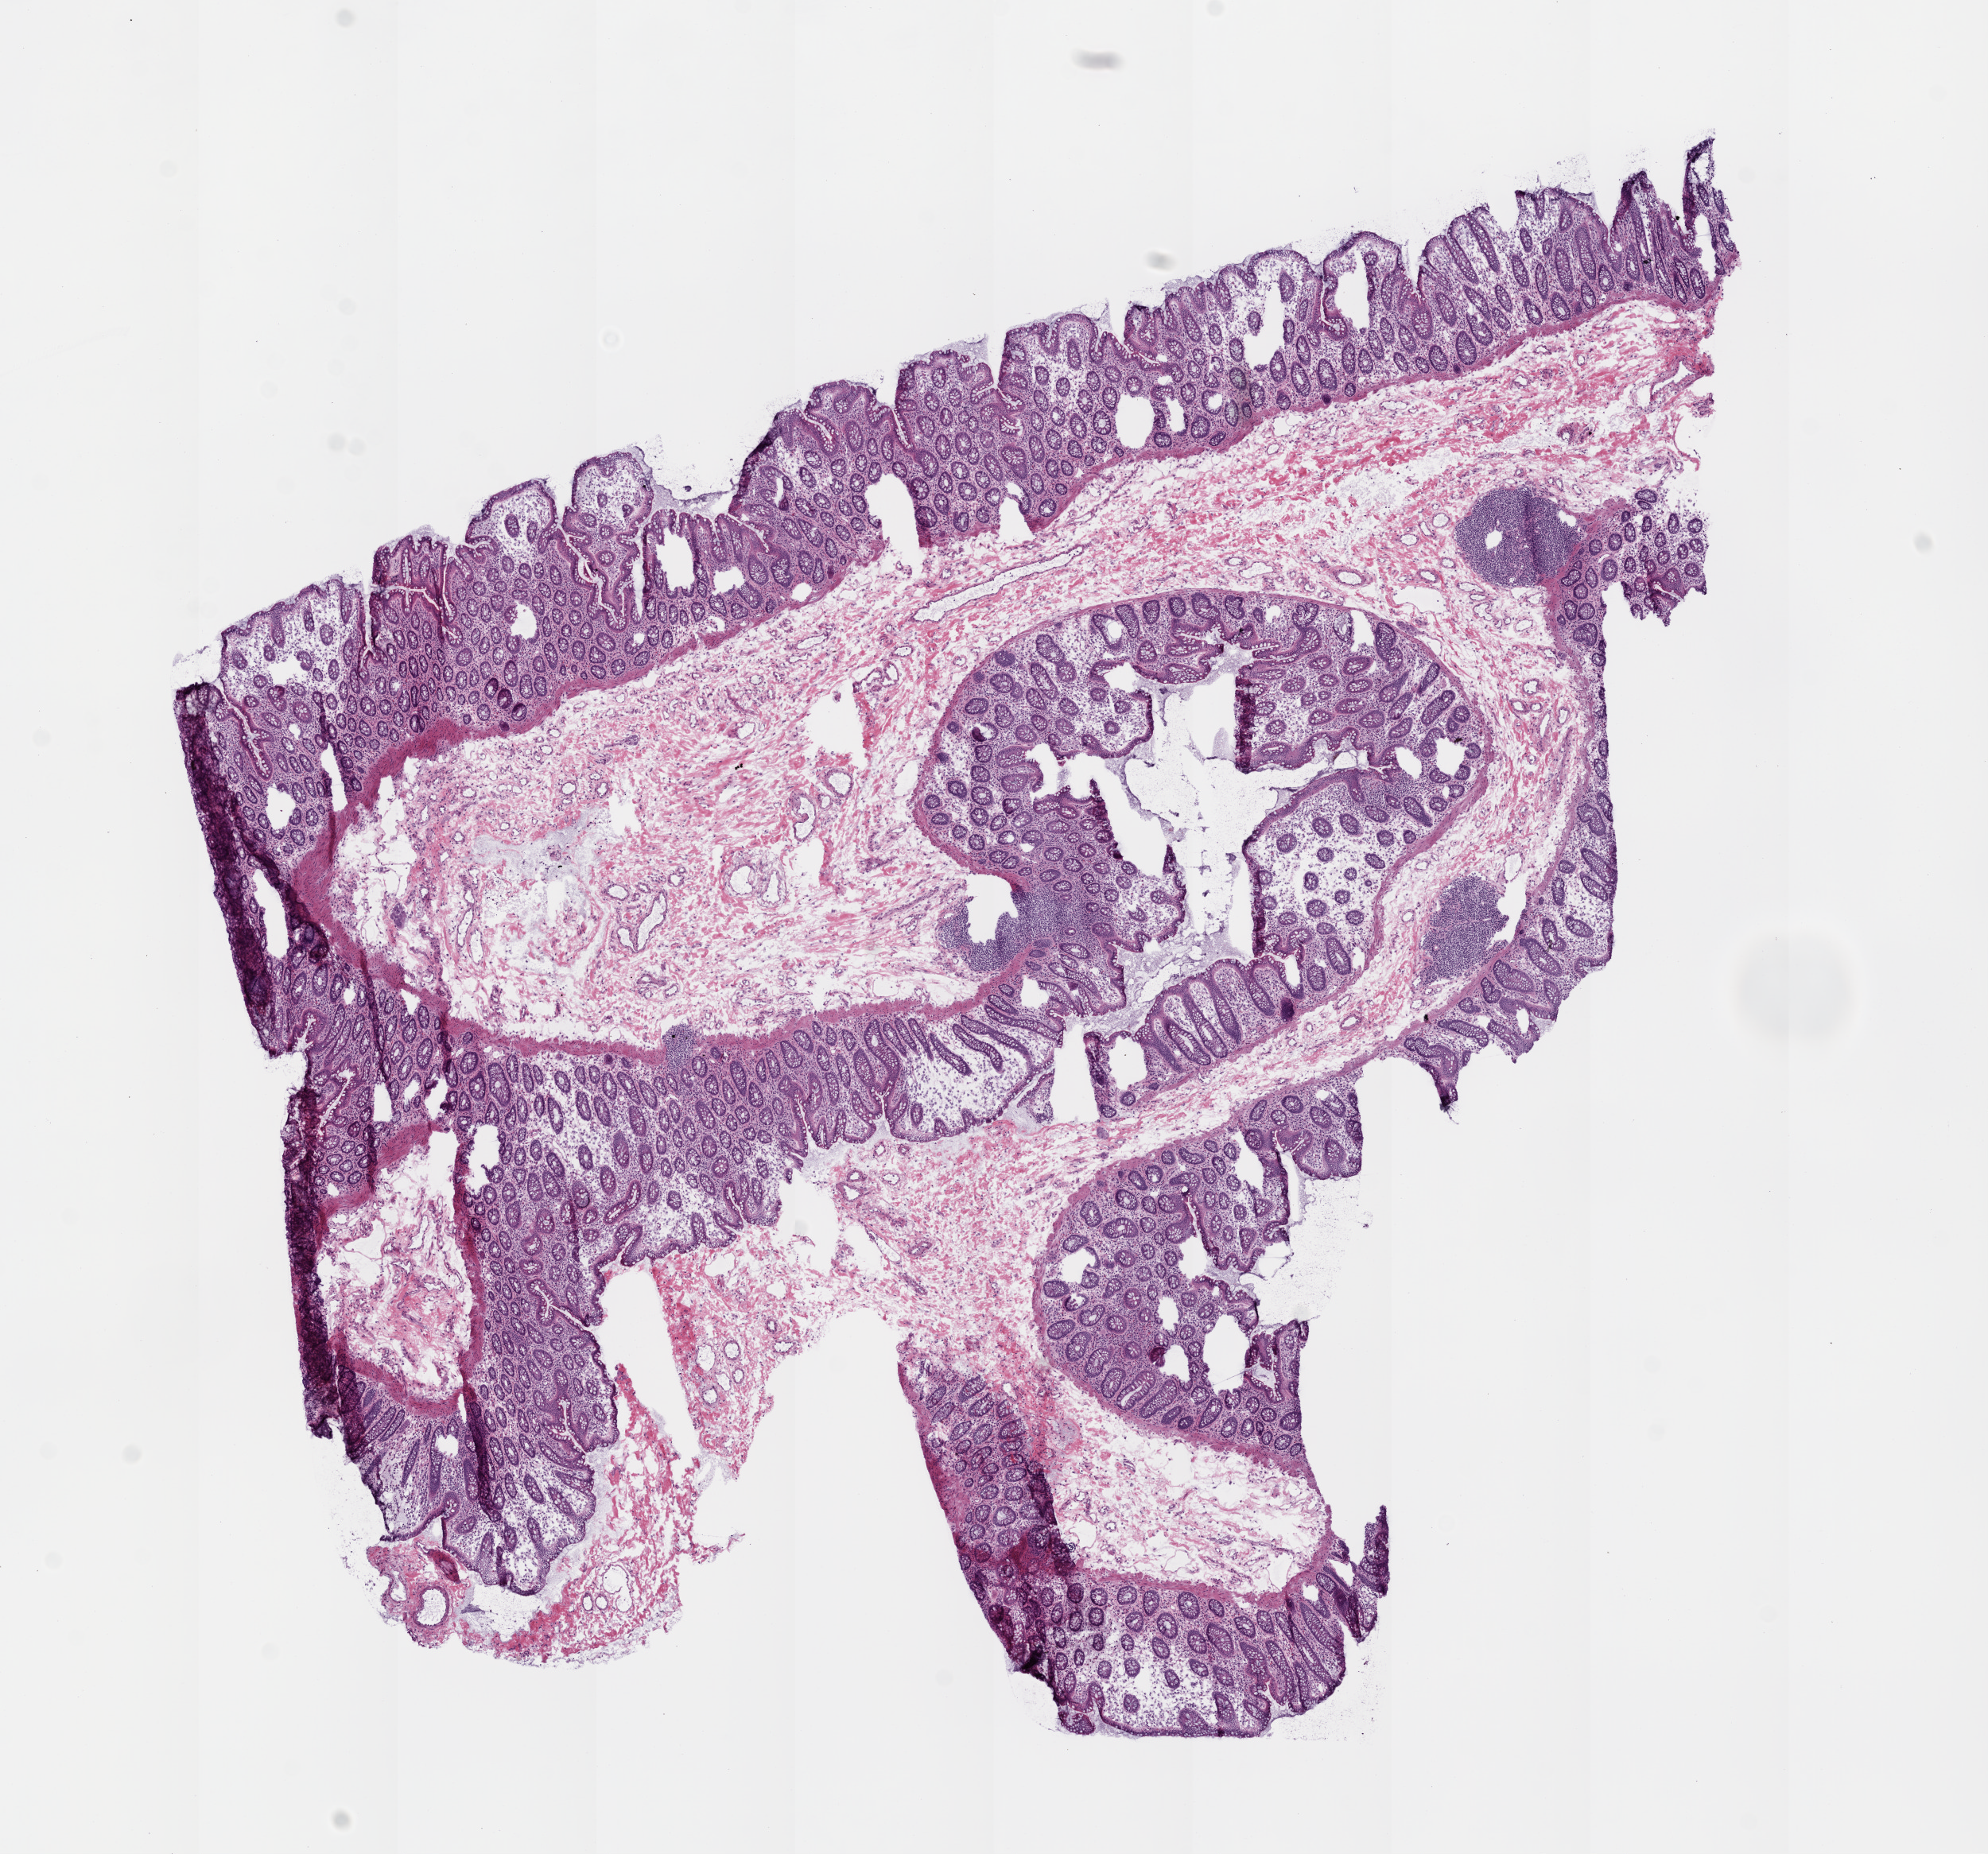
Hematoxylin and eosin (H&E) stained whole-slide image — low-resolution overview of the scanned area, about 10.0 x 9.4 mm (slide scanned at 20x), frozen section, sample: solid tissue normal (non-tumour tissue), colon. Female, age 75 years at initial diagnosis.
This section: solid tissue normal sample (biorepository sample class). Patient diagnosis: Adenocarcinoma, NOS.